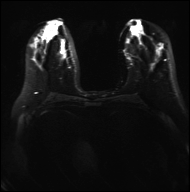
Breast MRI, one axial slice. Slice 13 of 40 in the series (ordered by position). Diffusion-weighted series; image 2 of 4 stored at this slice position (different b-values; order by instance number). 3 T. 4 mm slice thickness. 190 × 192 image matrix. Female patient.
Outlined on this slice (expert manual segmentation):
- tumour on diffusion-weighted imaging: bounding box [x1, y1, x2, y2] px = [46, 48, 63, 57]